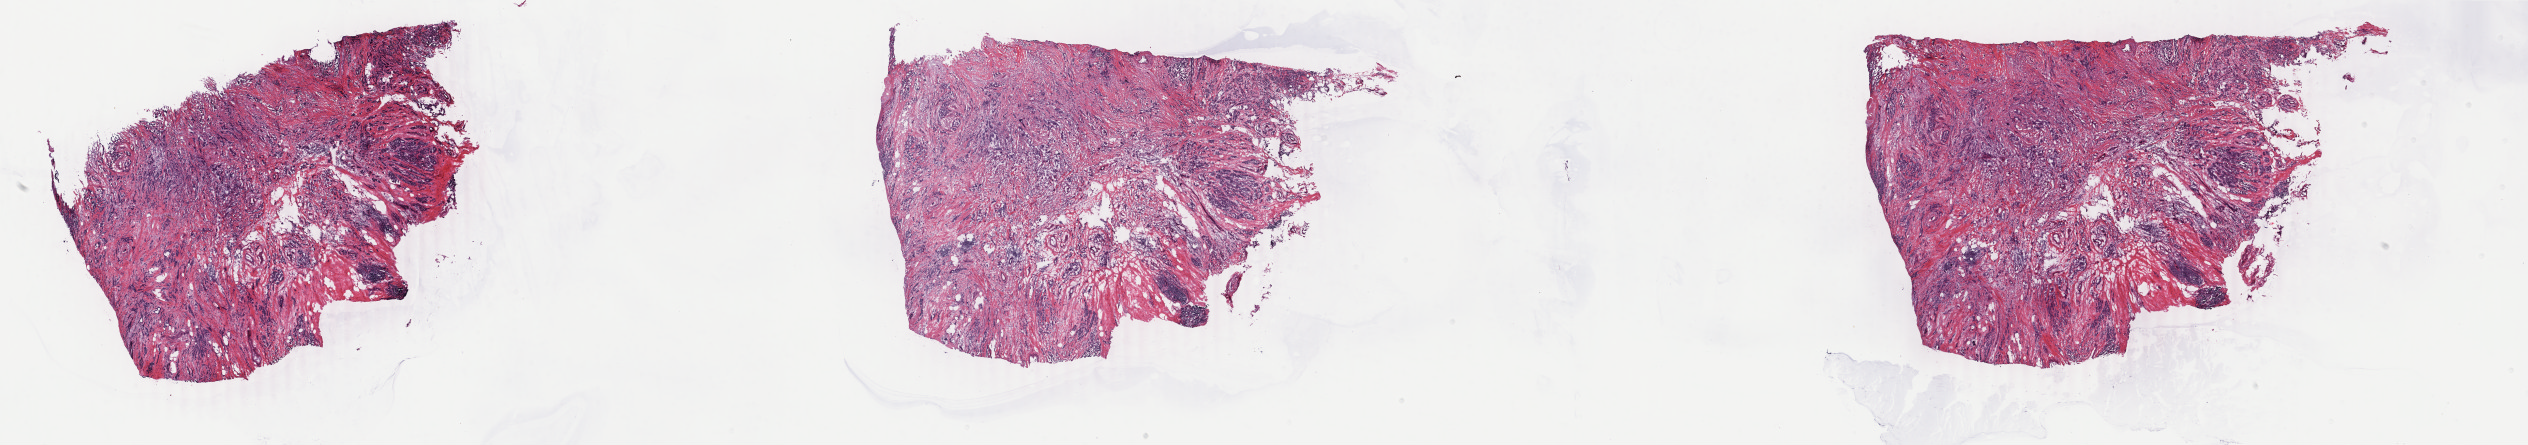
H&E-stained whole-slide image, a low-resolution overview of the entire scanned area, about 40.2 x 7.1 mm; frozen section; sample: primary tumour, breast. Female patient; age at initial diagnosis 74 years.
Pathologic diagnosis: Lobular carcinoma, NOS.